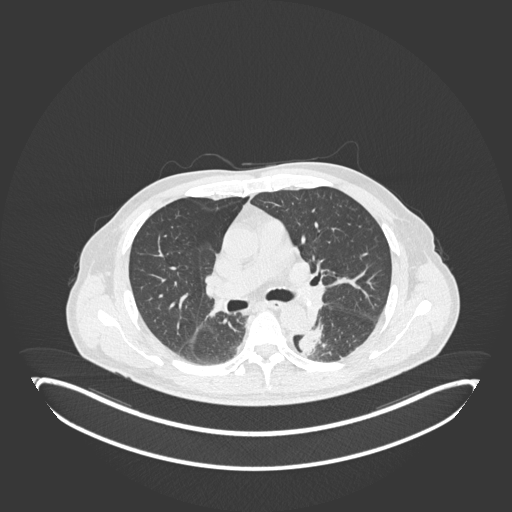
Chest CT, one axial slice; slice 126 of 251 in the series (ordered by position); reconstruction kernel B30f; 120 kVp; lung window (W 1500 / L -600 HU); 512 × 512 image matrix, field of view 500 × 500 mm. Patient: male, 72 years. Case-level facts recorded for this patient, not image findings: clinical TNM (as recorded): T2b N0 M1.
Structures marked on this image (bounding box drawn by a radiologist):
- lung tumour (recorded histology: adenocarcinoma): bounding box (x1, y1, x2, y2) in pixels: (293, 321, 330, 359)